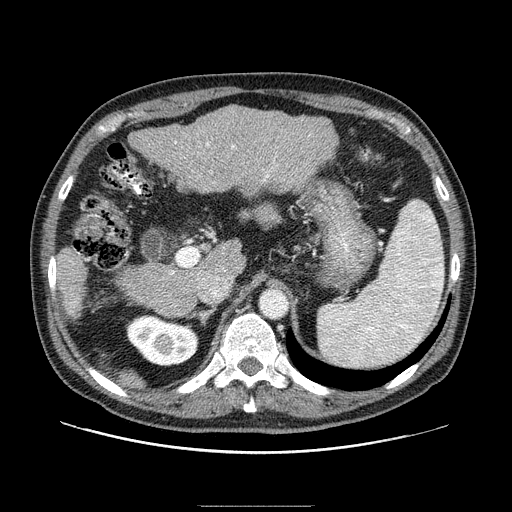
Contrast-enhanced abdominal CT (liver protocol), one axial slice; slice 51 of 99 in the series (ordered by position); reconstruction kernel STANDARD; 100 kVp; one of 2 acquisitions stored at this slice position; soft-tissue window (W 400 / L 40 HU); 2.5 mm slice thickness; 512 × 512 image matrix, field of view 400 × 400 mm. Case-level facts recorded for this patient, not image findings: diagnosis: hepatocellular carcinoma (patient treated with transarterial chemoembolisation; whether this scan precedes or follows treatment is not stated here); TNM stage (as recorded): Stage-II; Child-Pugh class: A; tumour differentiation: well differentiated; tumour nodularity: multinodular.
Structures marked on this image (semi-automatic segmentation, software-assisted and operator-edited):
- liver parenchyma outside the tumour (the mass and vessels are separate outlines, so this box may not span the whole liver): bounding box <56,106,338,321> (left, top, right, bottom; pixels)
- liver vessels: <174,141,273,181>